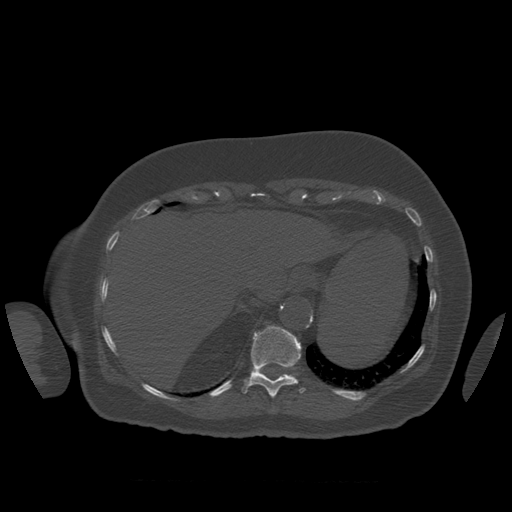
CT including the spine, one axial slice; slice 321 of 399 in the series (ordered by position); bone window (W 1800 / L 400 HU); 1.25 mm slice thickness; 512 × 512 image matrix, field of view 404 × 404 mm. Patient age 81 years. Case-level facts recorded for this patient, not image findings: primary cancer: renal; vertebrae with lytic lesions (as recorded): L1.
Structures marked on this image (semi-automatic segmentation, software-assisted and operator-edited):
- T11 vertebra: bounding box [x1, y1, x2, y2] px = [242, 326, 306, 398]